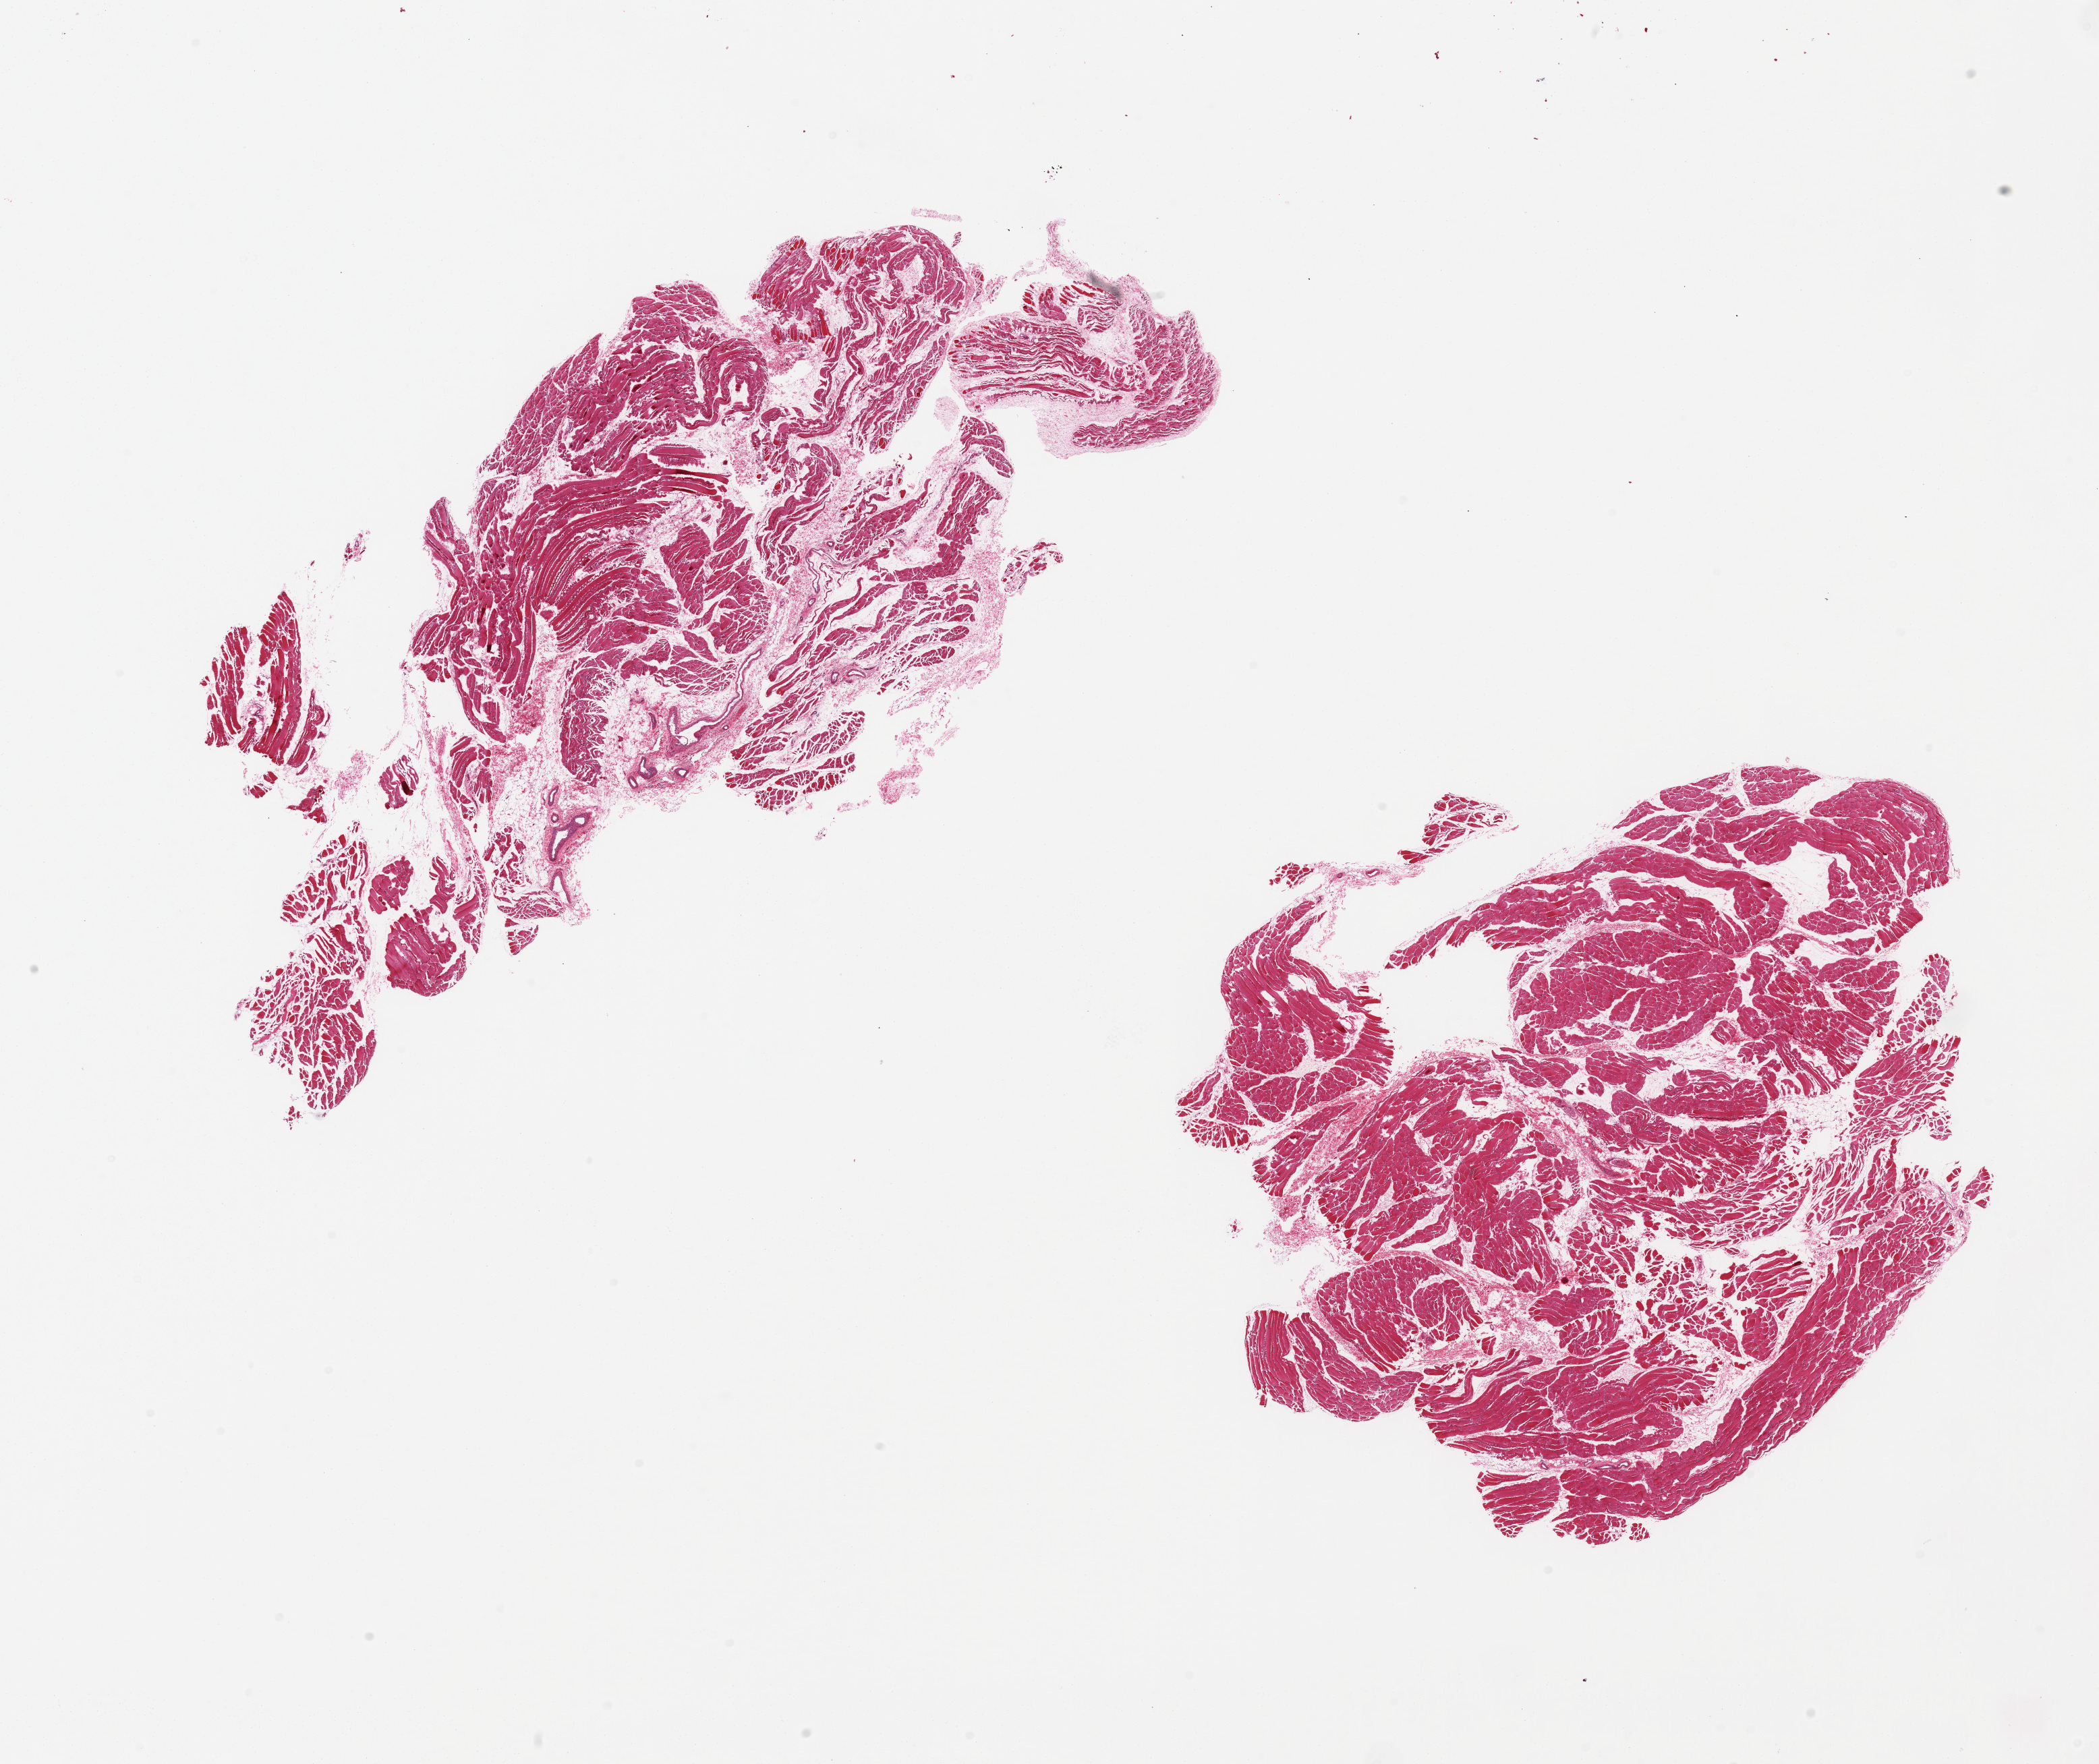
Whole-slide image, hematoxylin and eosin (H&E) stain, brightfield, low-resolution overview of the scanned area, about 24.6 x 20.7 mm (acquisition: 20x scan); PAXgene-fixed paraffin-embedded (PFPE) section; target tissue: skeletal muscle; donor tissue sample. Donor sex: female.
• reviewer comment on this tissue sample: 2 pieces, myo-atrophy; interstitial fat/fibrous tissue up to ~40%